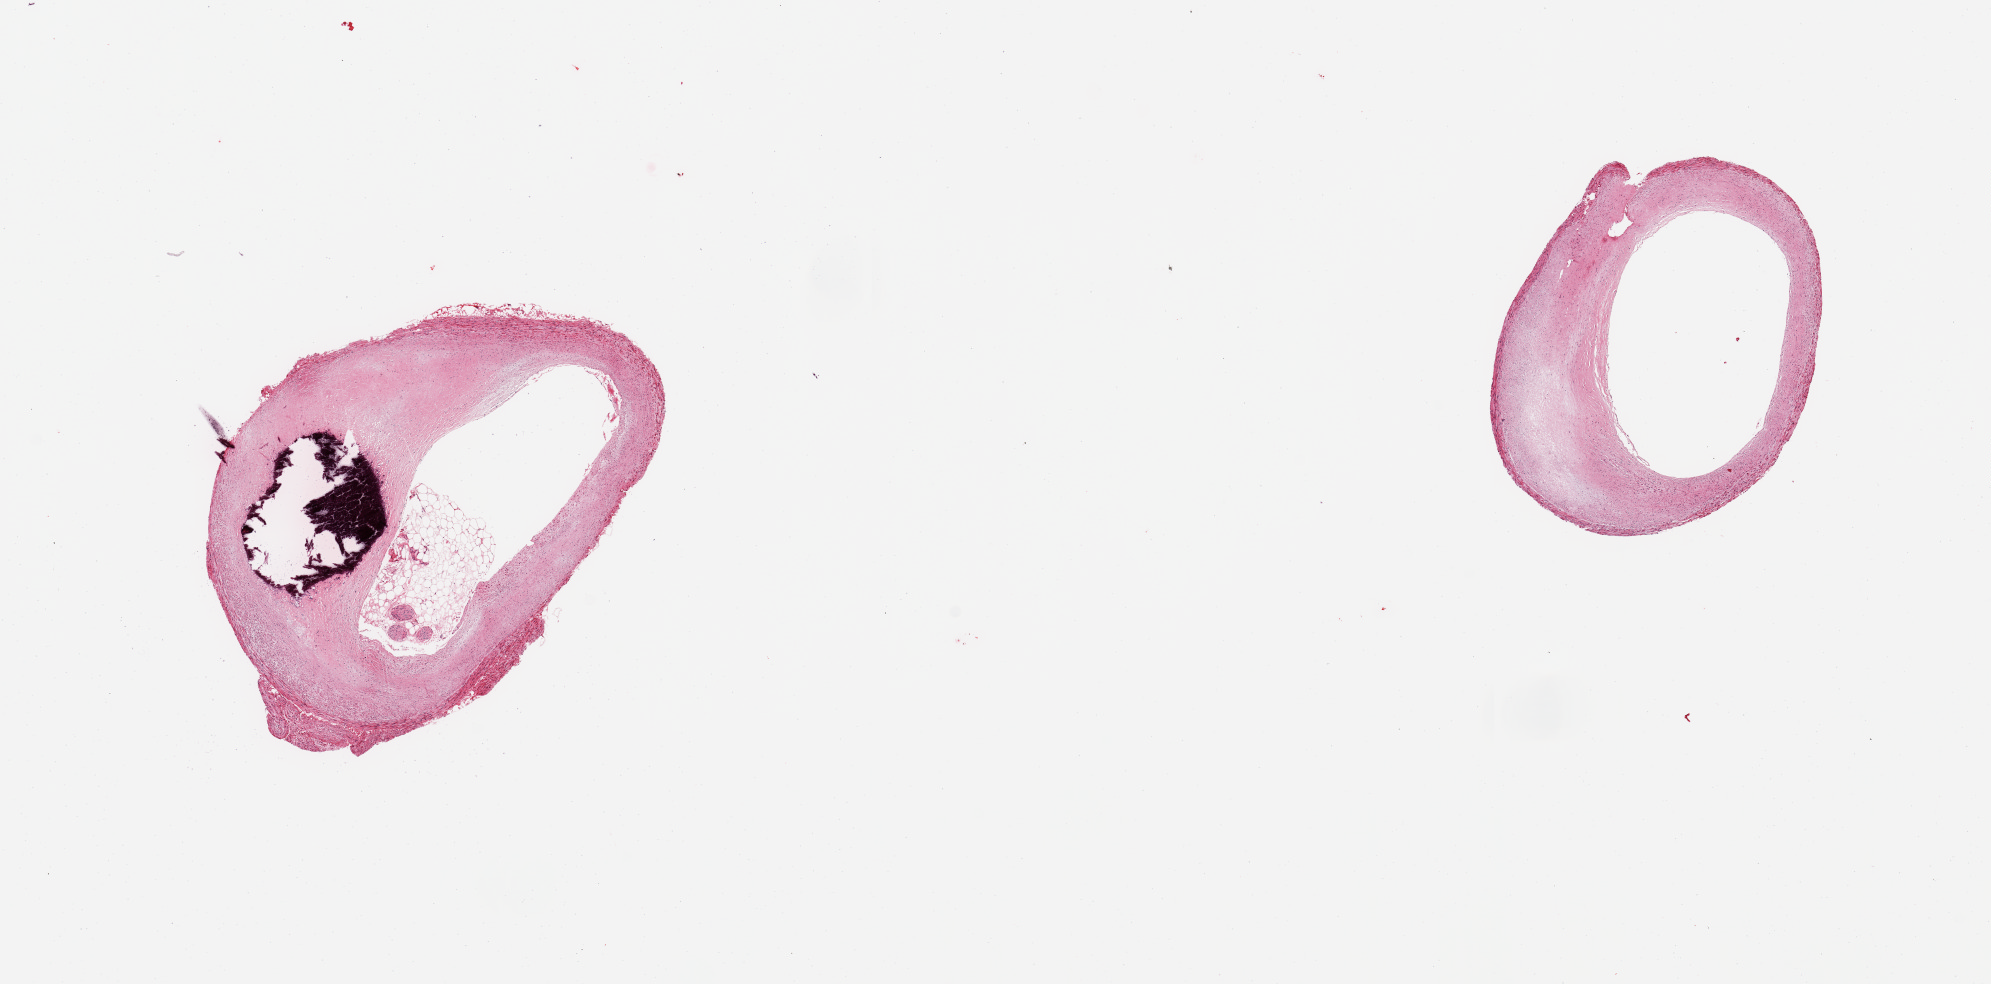
Digitized H&E-stained section — shown as a low-resolution overview of the whole scanned area (about 15.8 x 7.8 mm, acquisition: 20x scan); PAXgene-fixed paraffin-embedded (PFPE) section; section of coronary artery (target tissue); tissue donor sample. Male donor.
- reviewer comment on this tissue sample: 2 pieces, 70% calcifying occlusive atherosis